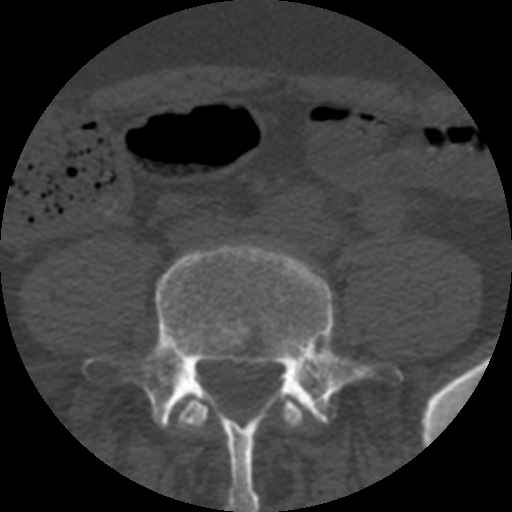
CT including the spine, one axial slice. Reconstruction kernel STANDARD. 120 kVp. Bone window (W 1800 / L 400 HU). 512 × 512 image matrix, field of view 160 × 160 mm. Patient age 57 years. Case-level facts recorded for this patient, not image findings: primary cancer: prostate.
Outlined on this slice (semi-automatically segmented with operator editing):
- L4 vertebra: bounding box [x1, y1, x2, y2] px = [178, 394, 304, 429]
- L5 vertebra: [84, 245, 402, 512]